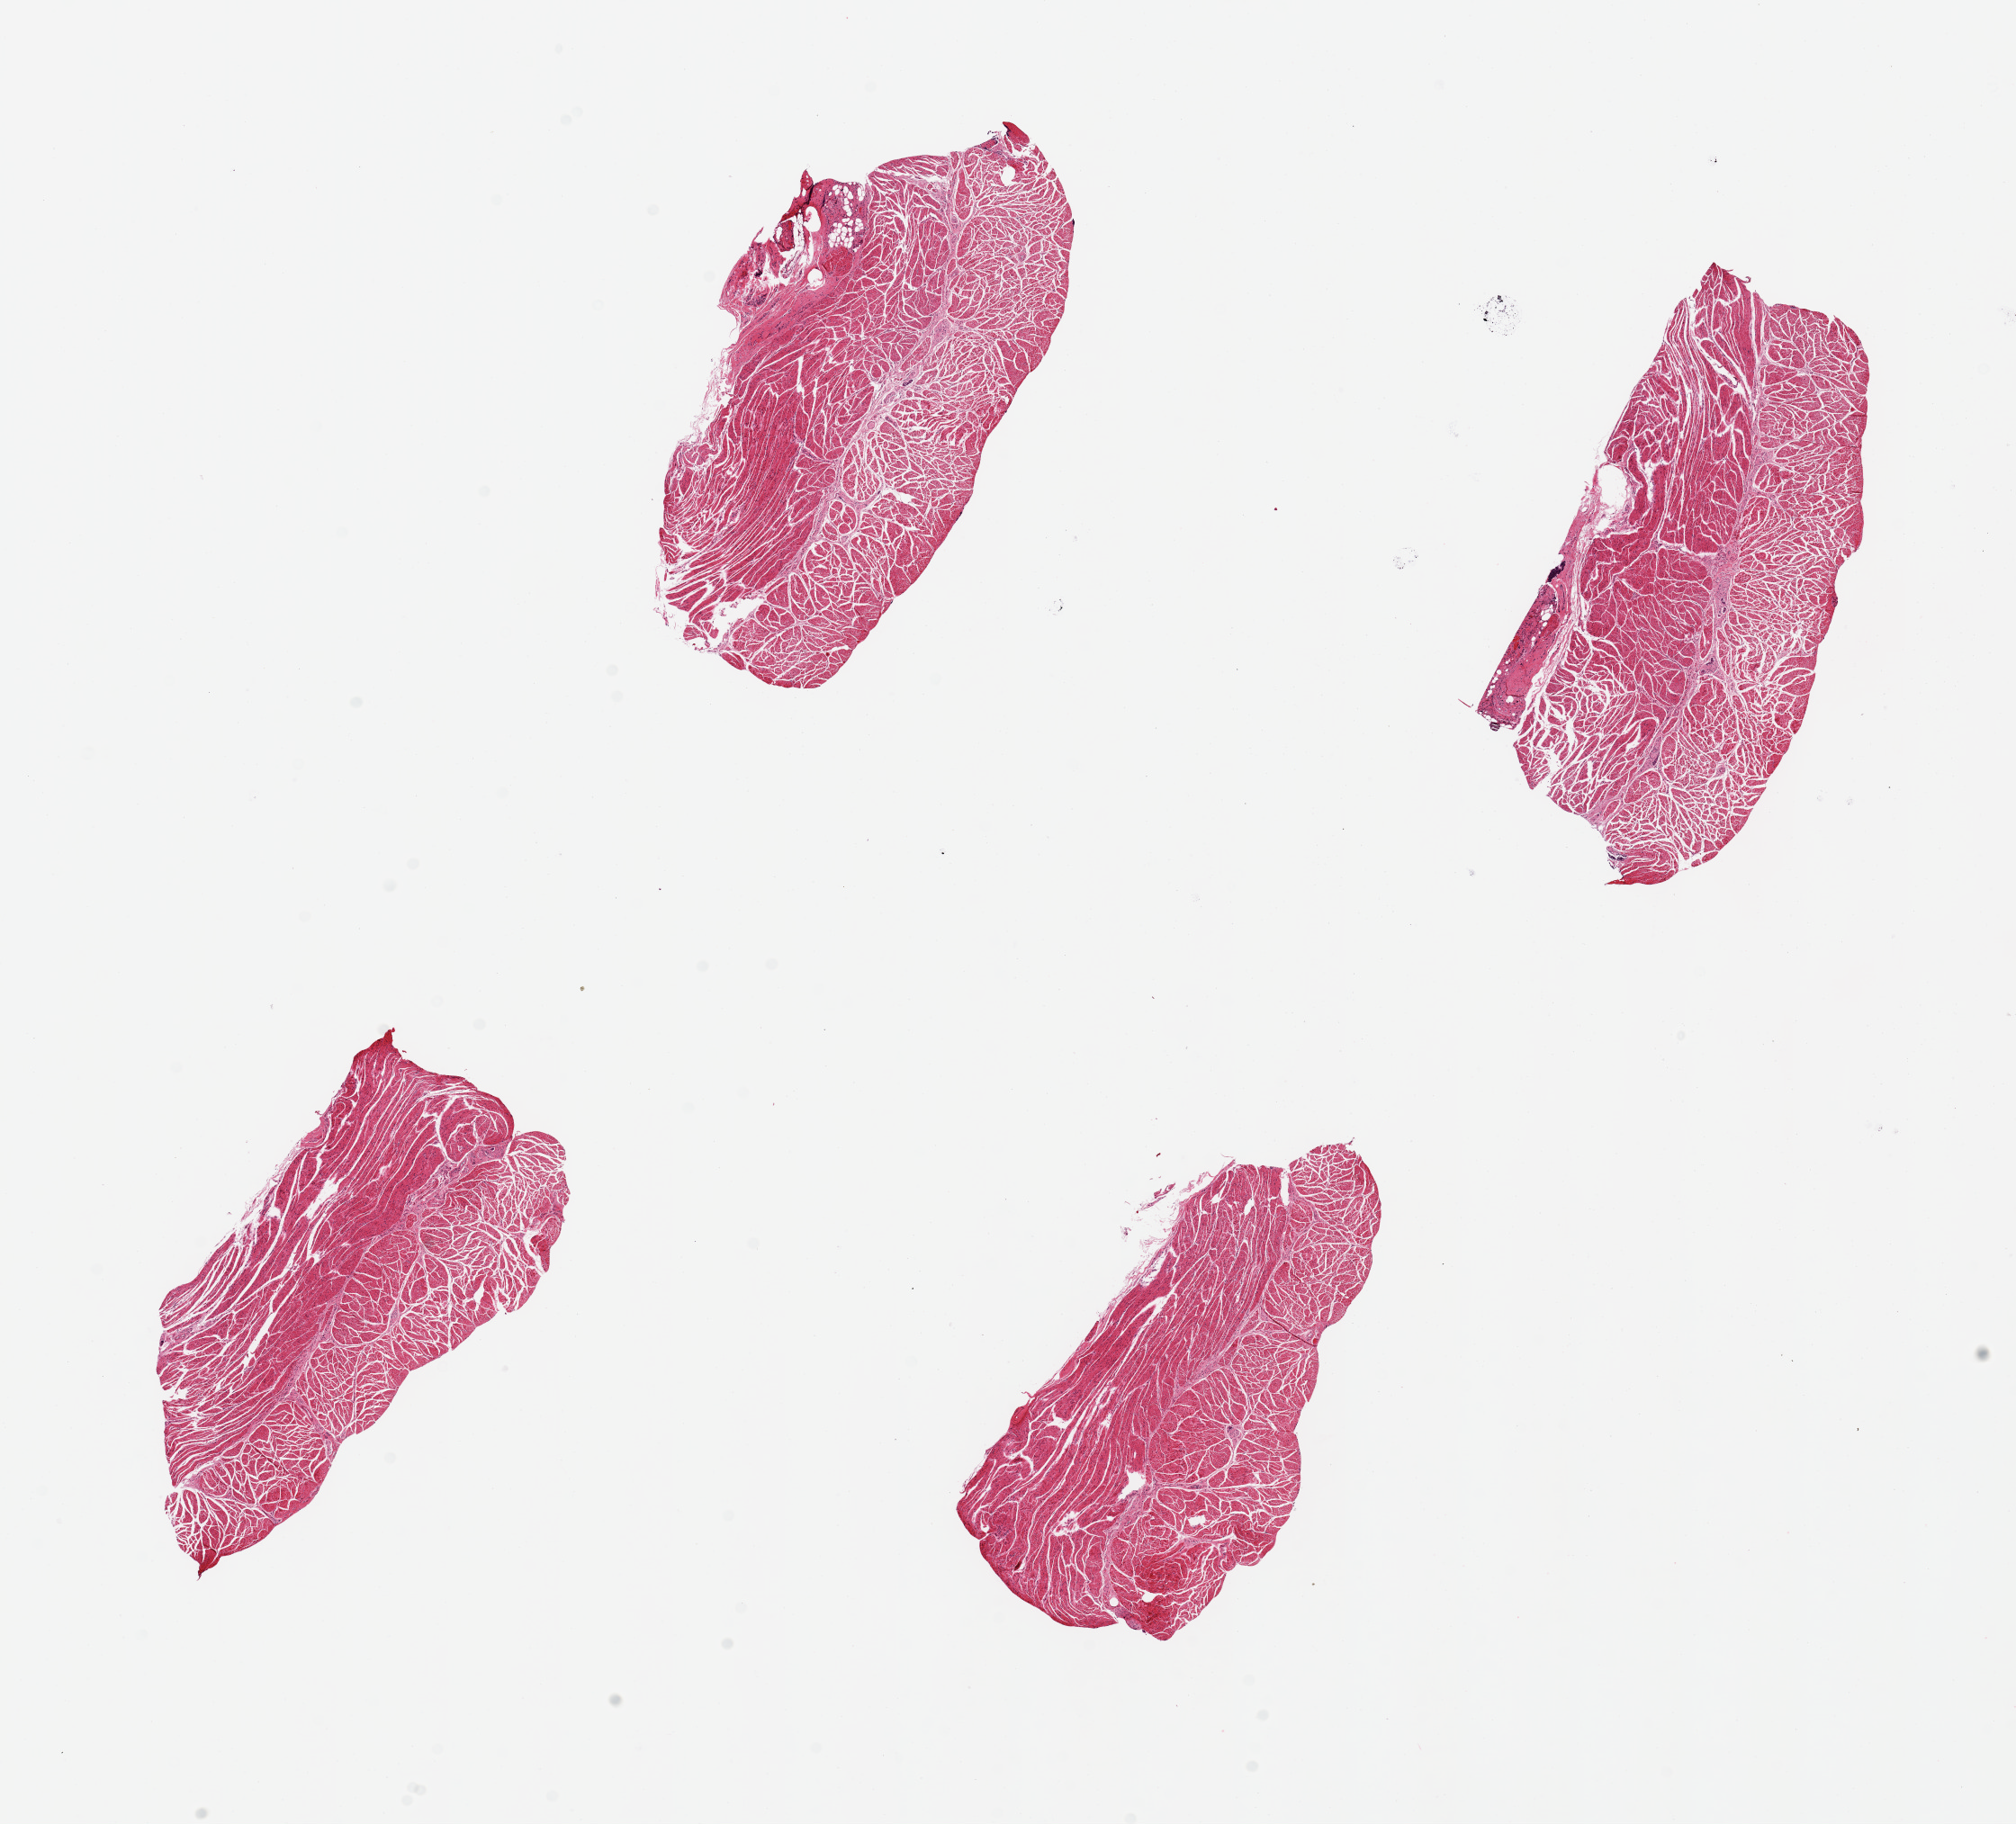
Whole-slide image, H&E stain, whole scanned area (about 17.7 x 16.0 mm, slide scanned at 20x) shown as a low-resolution overview; PAXgene-fixed, paraffin-embedded tissue; section of esophageal muscle (target tissue); donor tissue sample.
- pathologist's review note for this sample: 4 pieces, up to 5x2.5mm